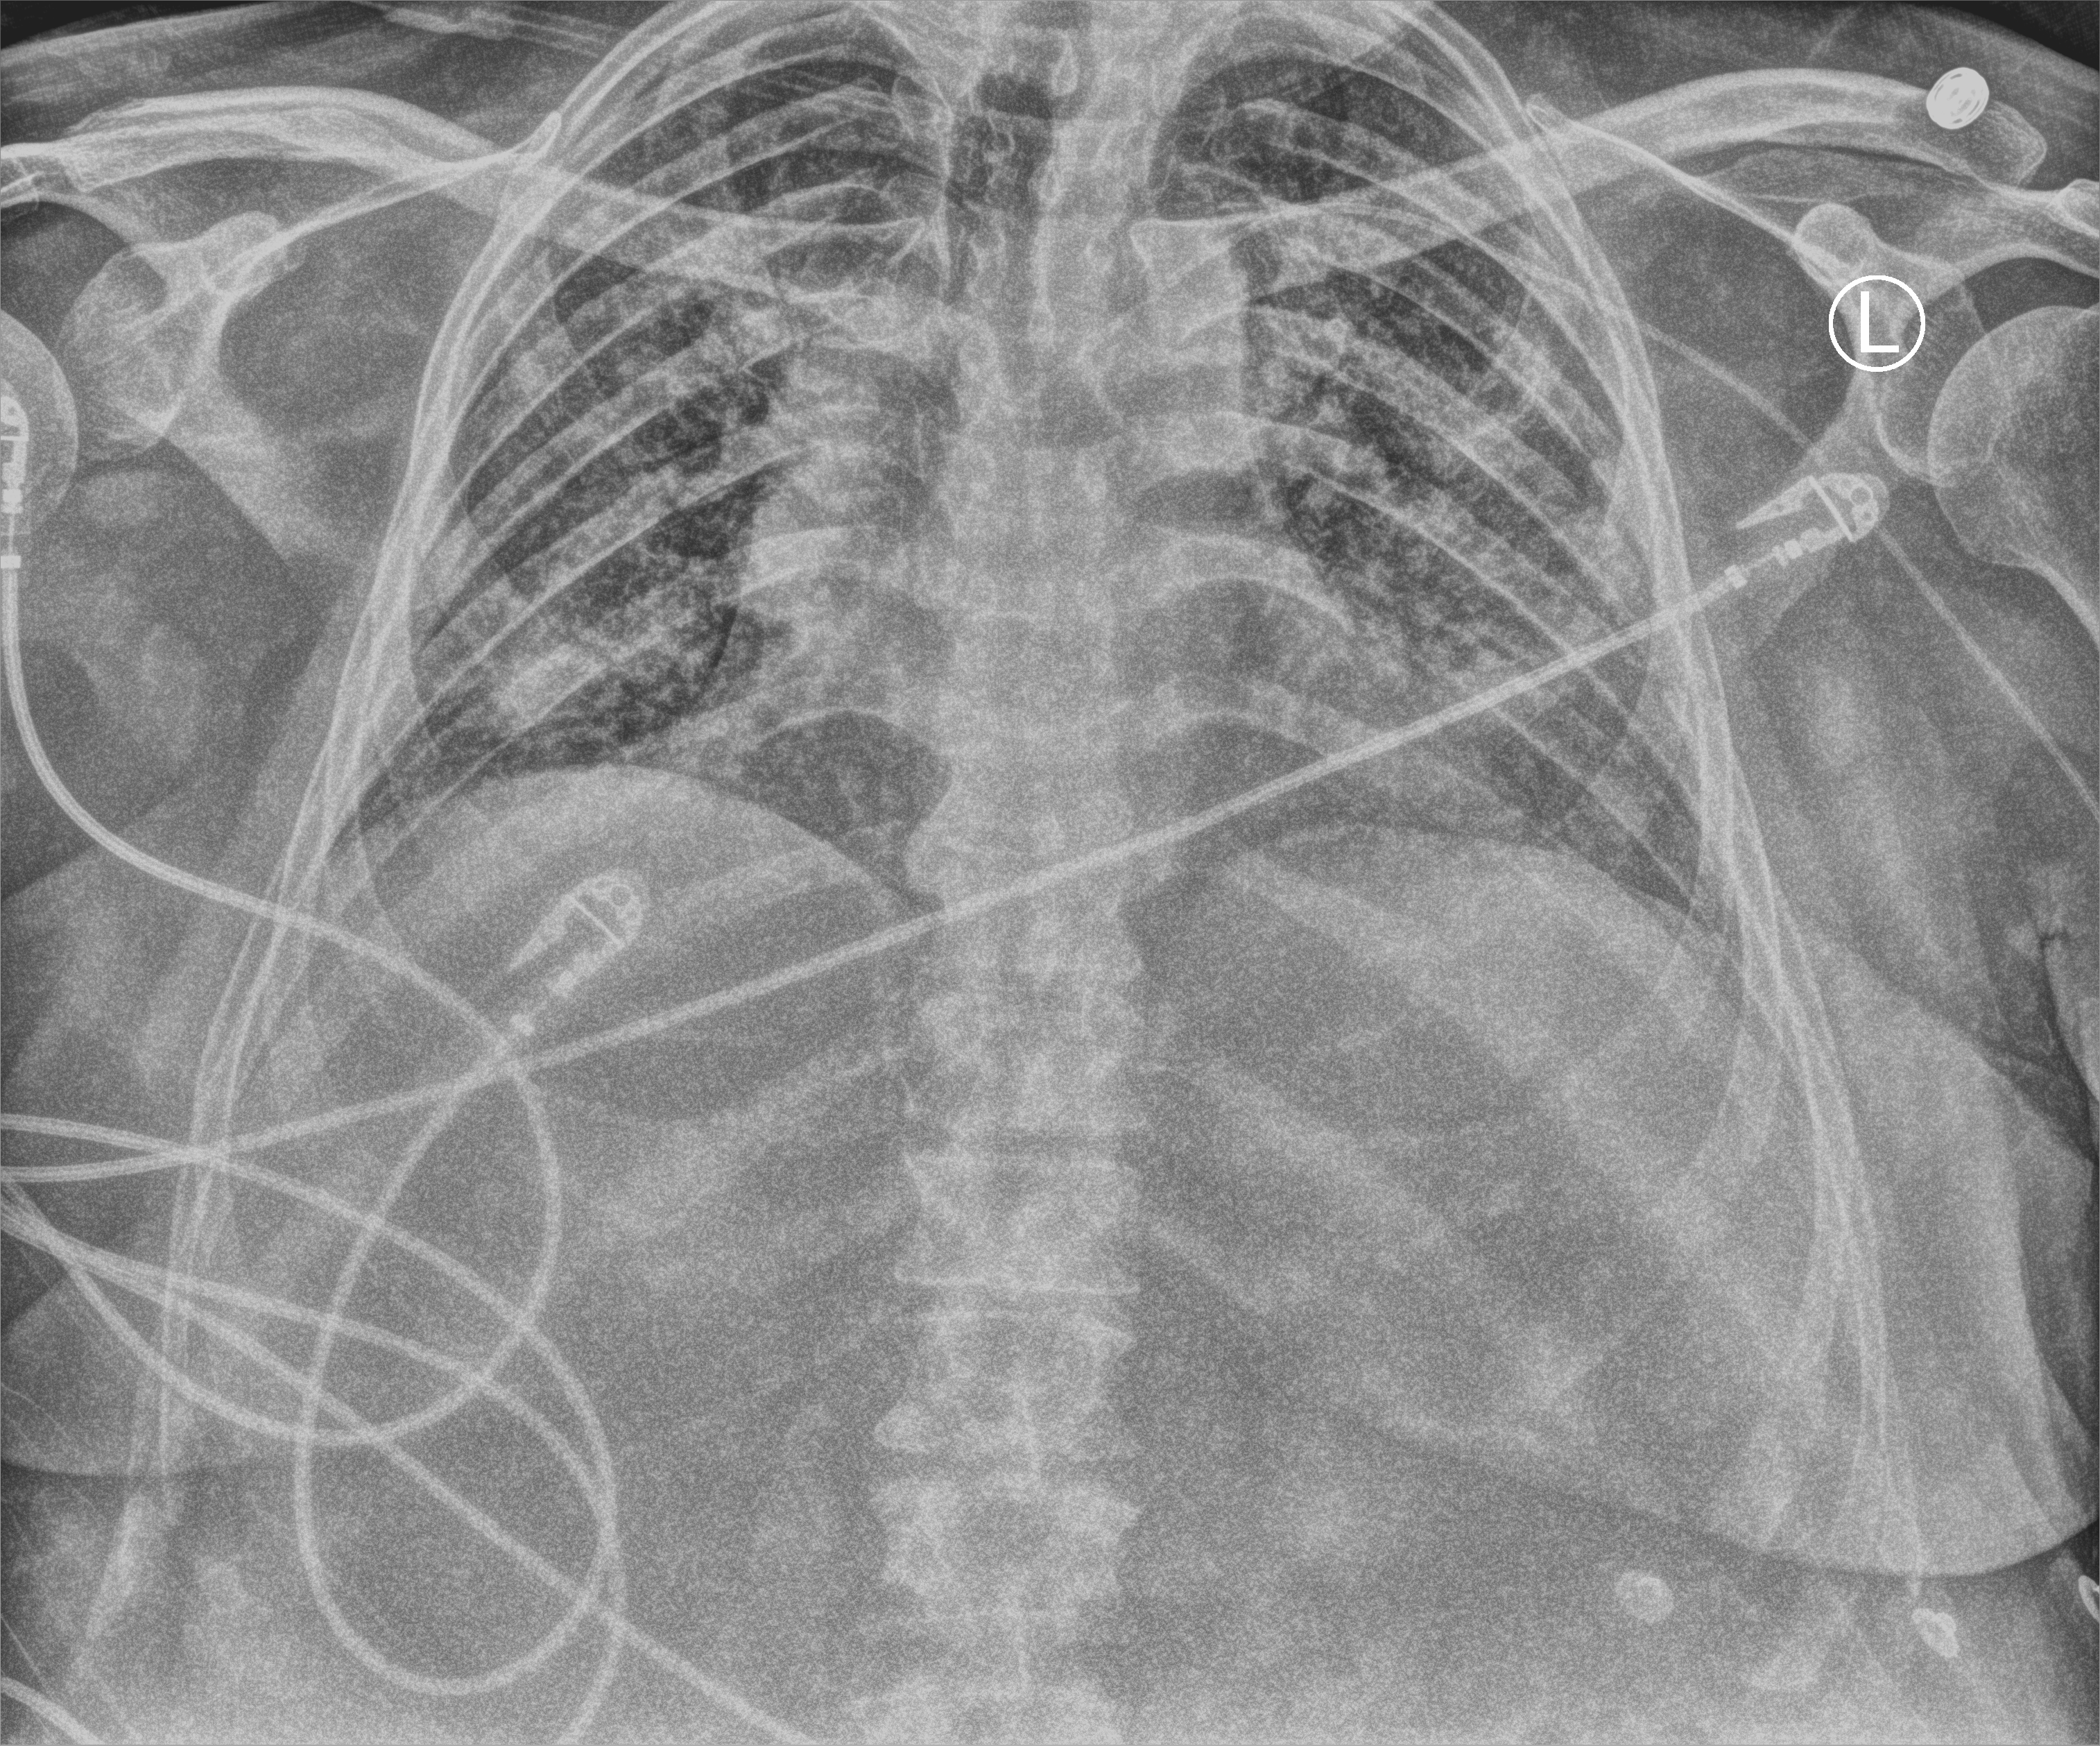
Portable chest radiograph; anteroposterior (AP) projection. Male patient hospitalised with COVID-19, age 18–59 years.
Hospital-stay facts (about this admission, not read from this image; timing relative to this image not recorded): admitted to intensive care during this hospital stay: yes.